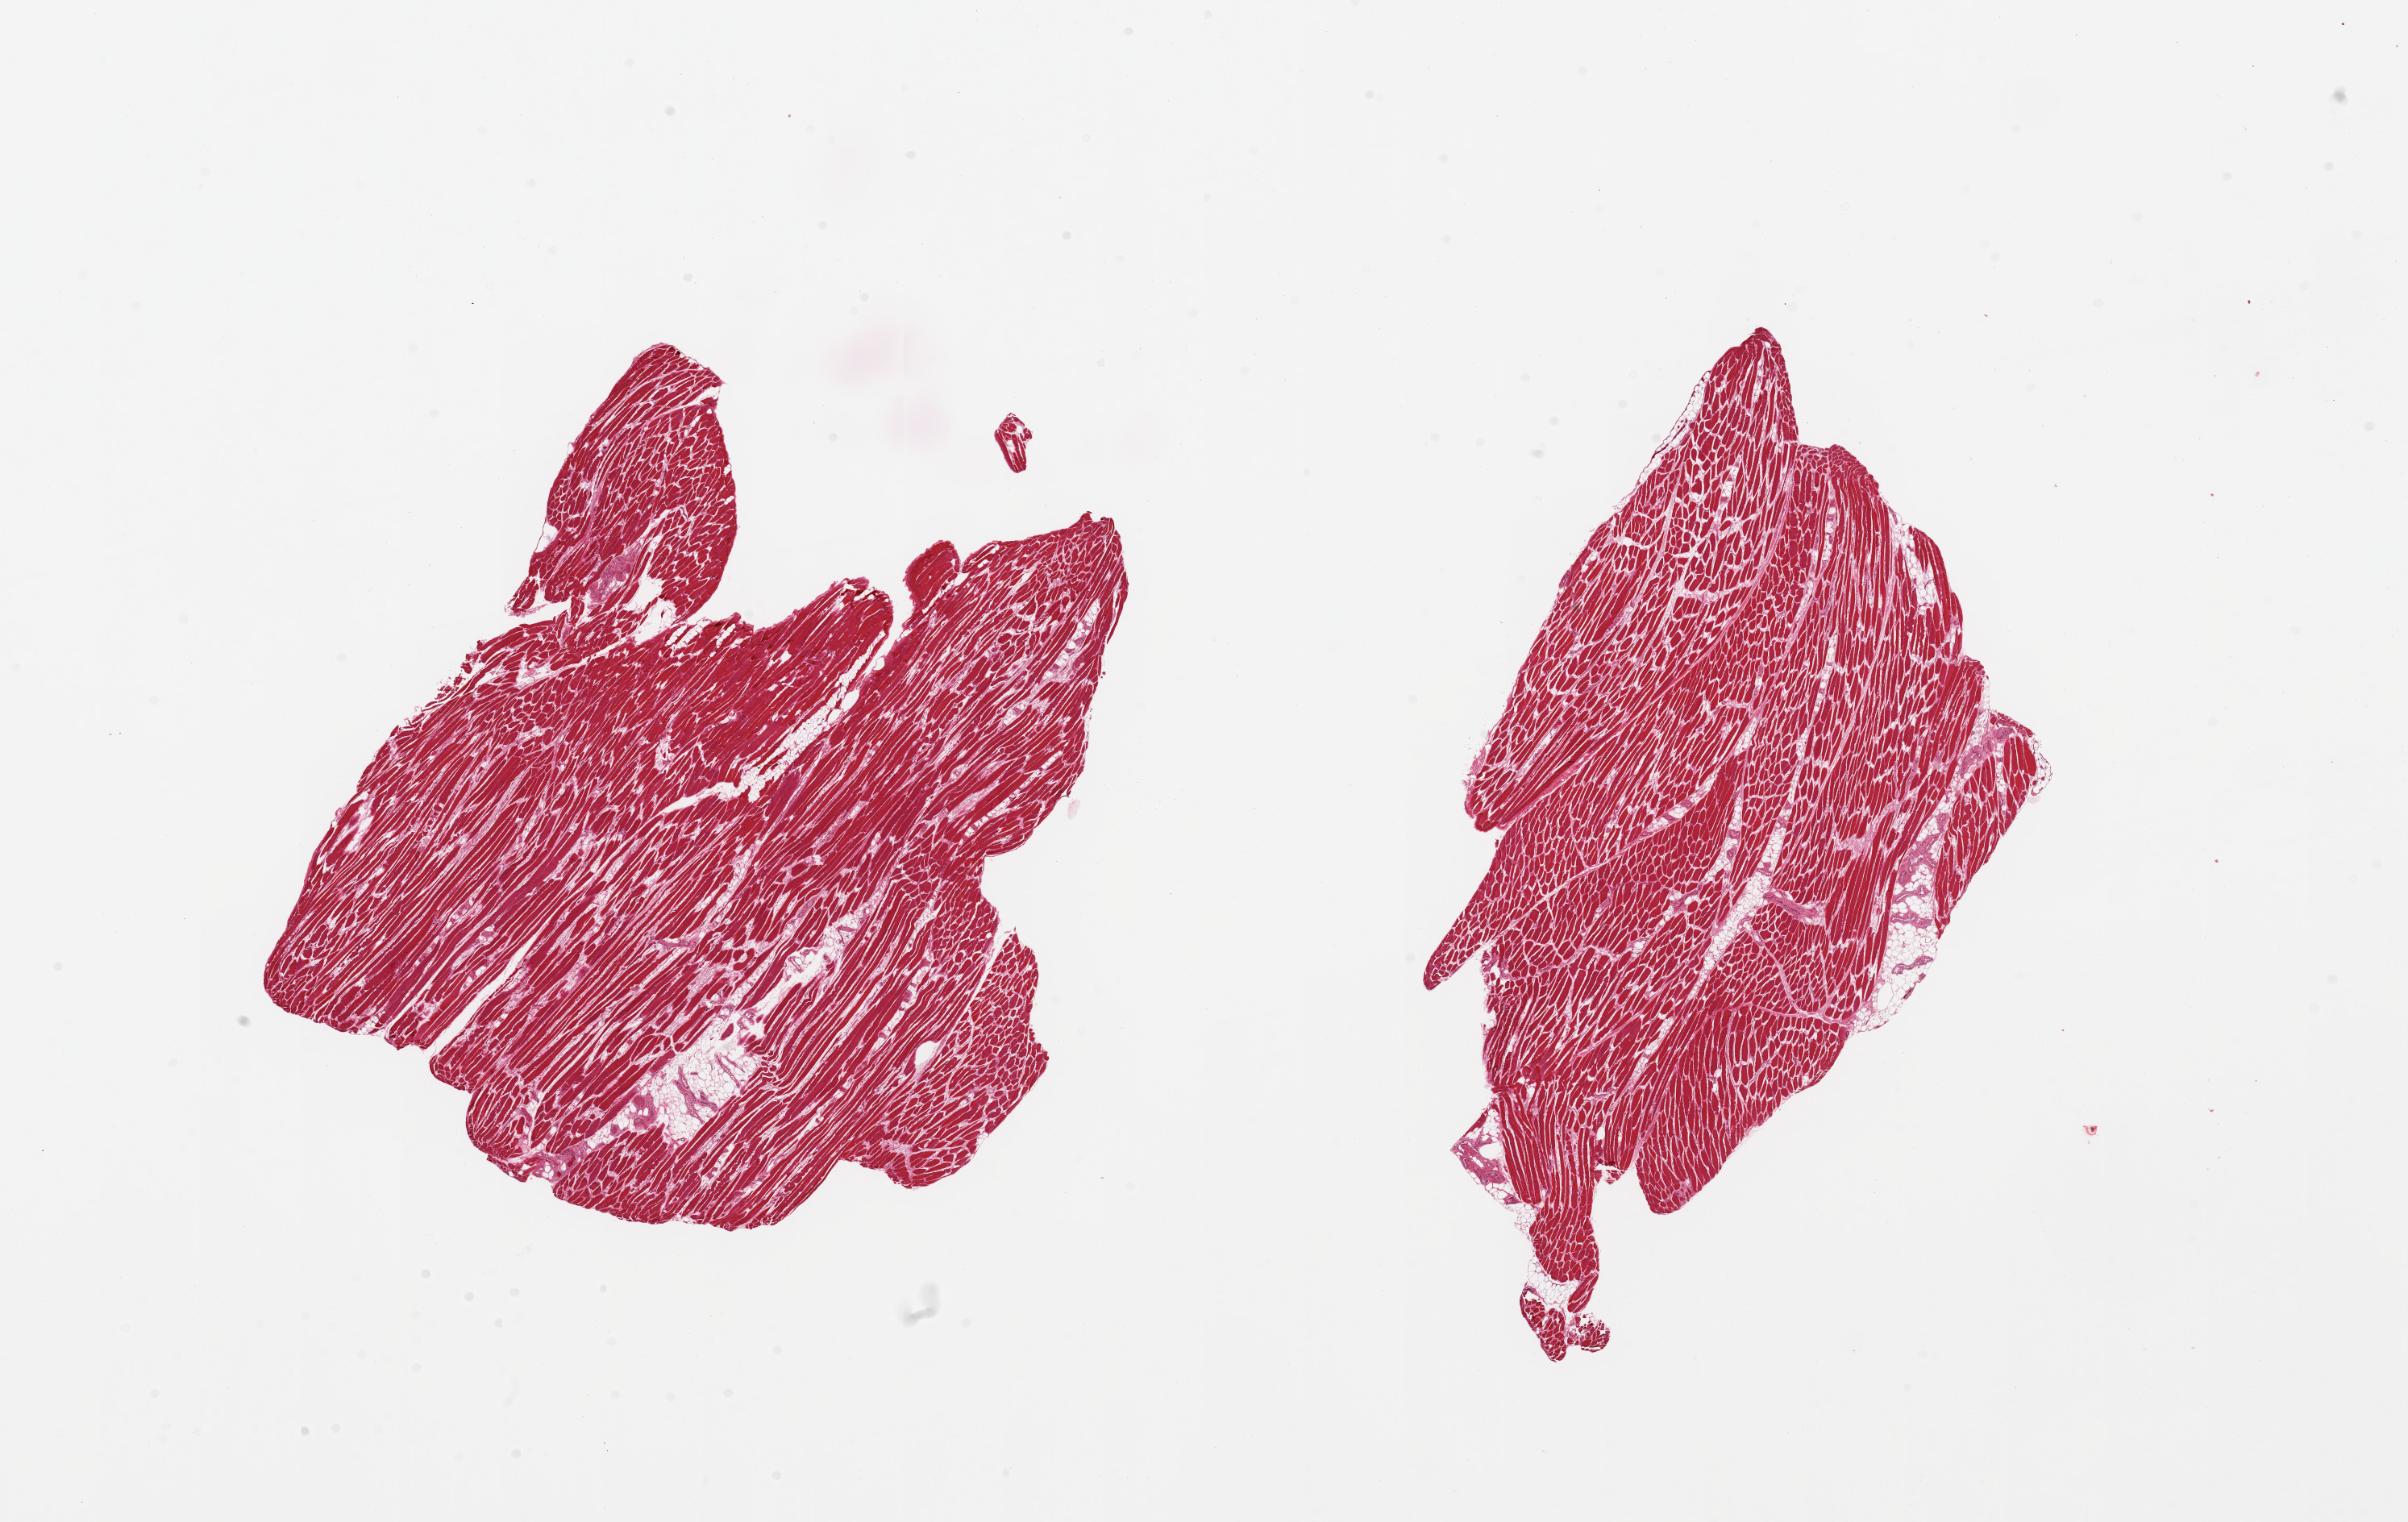
Hematoxylin and eosin (H&E) whole-slide image — a low-resolution overview of the entire scanned area, about 23.6 x 14.9 mm (from a 20x scan), PAXgene-fixed, paraffin-embedded tissue, section of skeletal muscle (target tissue), donor tissue sample.
- reviewer comment on this tissue sample: 2 pieces; 5% internal fat